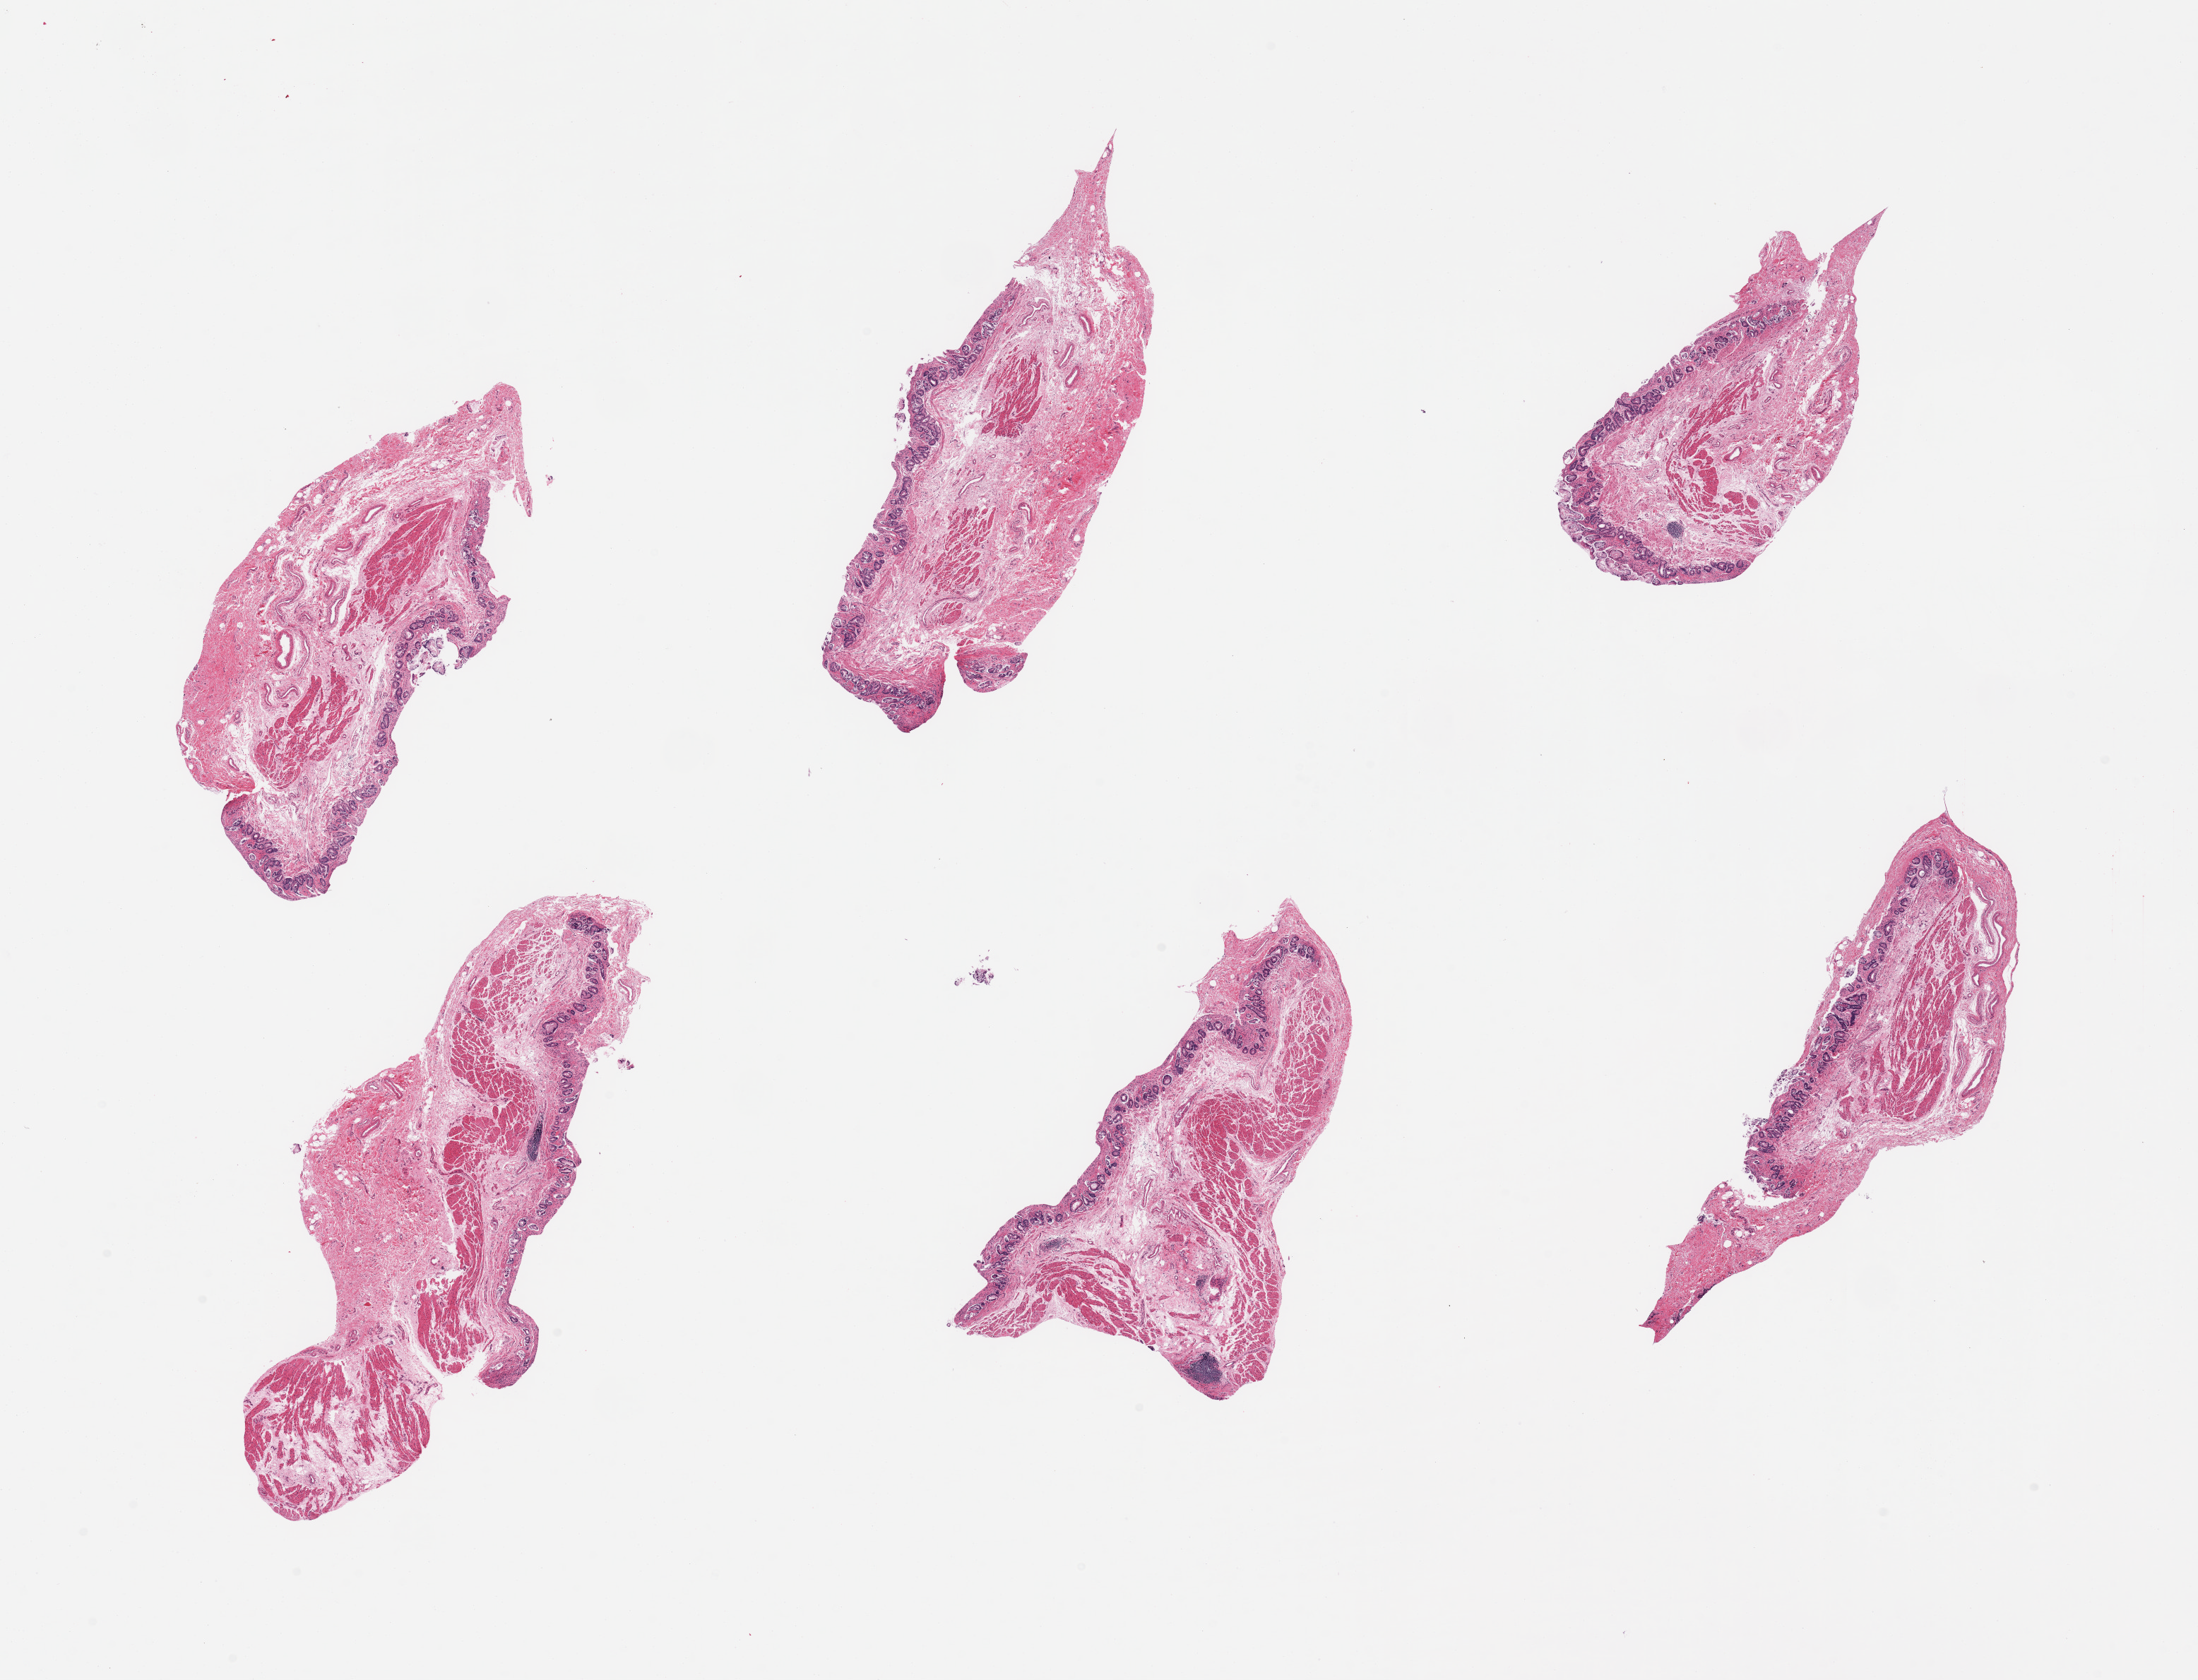
Whole-slide image, haematoxylin and eosin stain, shown as a low-resolution overview of the whole scanned area (about 24.6 x 18.8 mm, acquisition: 20x scan); PAXgene-fixed, paraffin-embedded tissue; sampled site (target tissue): esophageal mucous membrane; donor tissue sample. Male donor.
Pathologist's review note for this sample: 6 pieces, mucosa sloughing; no squamous mucosa, extensive intestinal/Barrett metaplasia.